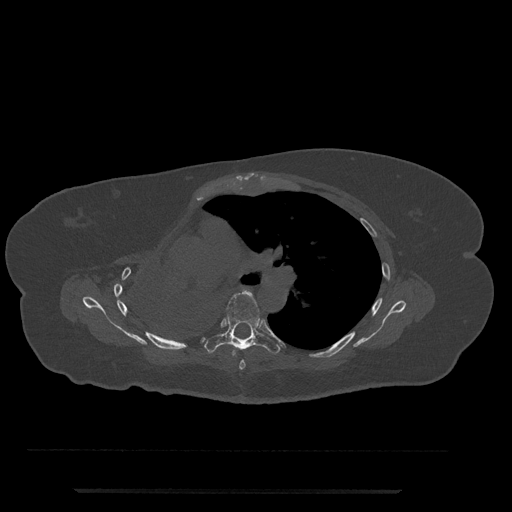
CT including the spine, one axial slice. Position 504 of 797 along the scan axis. 120 kVp. Bone window (W 1800 / L 400 HU). 0.5 mm slice thickness. 512 × 512 image matrix, field of view 440 × 440 mm. Patient: female, 51 years. Case-level facts recorded for this patient, not image findings: primary cancer: neuro; vertebrae with lytic lesions (as recorded): T8.
Structures marked on this image (semi-automatically segmented with operator editing):
- T5 vertebra: bounding box (x1, y1, x2, y2) in pixels: (239, 360, 246, 370)
- T6 vertebra: (206, 292, 280, 358)